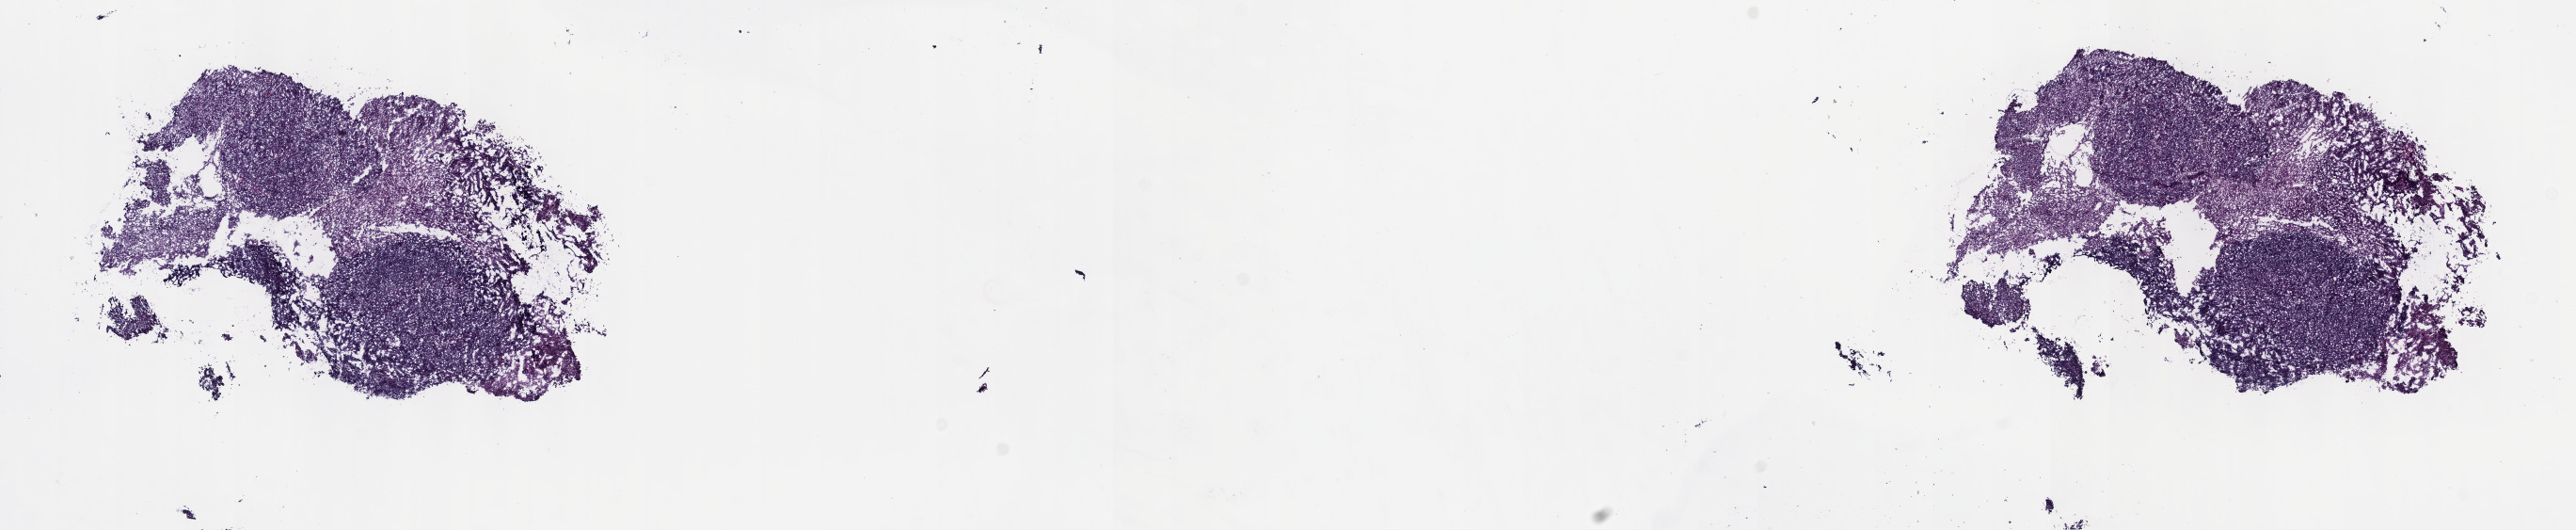
H&E whole-slide image — shown as a low-resolution overview of the whole scanned area (about 22.1 x 4.6 mm); frozen section from the top of the tissue portion; sample: primary tumour, thymus. Patient: female, age at initial diagnosis 72 years. Composition of this section per pathologist review: tumour cells 100%, tumour nuclei 80%, normal cells 0%, stromal cells 0%, necrosis 0%. Infiltration values recorded for this section: lymphocyte infiltration 1%, monocyte infiltration 0%, neutrophil infiltration 0%.
Pathologic diagnosis: Thymoma, type AB, malignant.